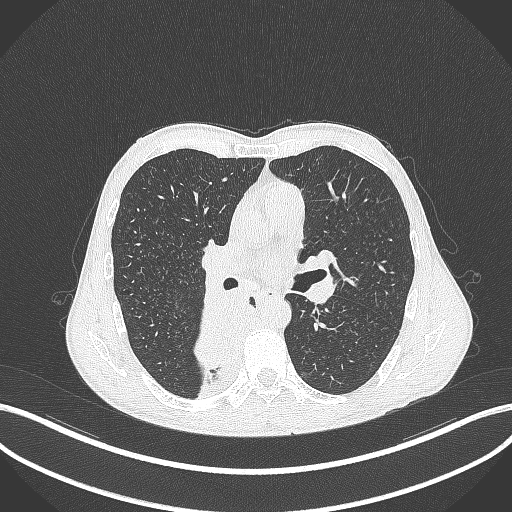
Chest CT, one axial slice. Position 212 of 371 along the scan axis. 120 kVp. Lung window (W 1500 / L -600 HU). 1 mm slice thickness. 512 × 512 image matrix, field of view 400 × 400 mm. Male patient, age 58 years. Case-level facts recorded for this patient, not image findings: clinical TNM (as recorded): T3 N1 M1.
Annotated regions visible in this slice (rectangle marked by the reading radiologist):
- lung tumour (recorded histology: squamous cell carcinoma): box from (x=183, y=290) to (x=248, y=367) px